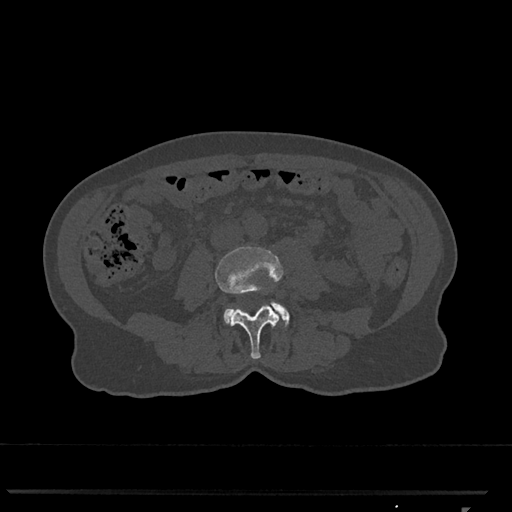
CT including the spine, one axial slice. Slice 252 of 793 in the series (ordered by position). Reconstruction kernel Br40s/3. 120 kVp. Bone window (W 1800 / L 400 HU). 0.5 mm slice thickness. 512 × 512 image matrix, field of view 380 × 380 mm. Female patient, age 62 years. From the clinical record (not read from this slice): primary cancer: renal.
Outlined on this slice (semi-automatic segmentation, software-assisted and operator-edited):
- L3 vertebra: bounding box <215,246,283,359> (left, top, right, bottom; pixels)
- L4 vertebra: <224,301,289,326>